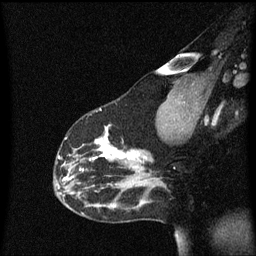
Breast MRI (dynamic contrast-enhanced), one sagittal slice; position 40 of 60 along the scan axis; dynamic contrast-enhanced series, image 2 of 3 at this slice position (ordered by acquisition); 1.5 T; TE 4.2 ms, TR 8.4 ms; 256 × 256 image matrix. Patient: female, 33 years.
Structures marked on this image (semi-automatically segmented with operator editing):
- analysis volume of interest (the breast-tissue region the enhancement analysis was run in; not a lesion): bounding box <54,120,152,191> (left, top, right, bottom; pixels)
- tumour enhancement mask (voxels above the 70 % enhancement threshold inside the analysis volume of interest): <59,126,151,181>